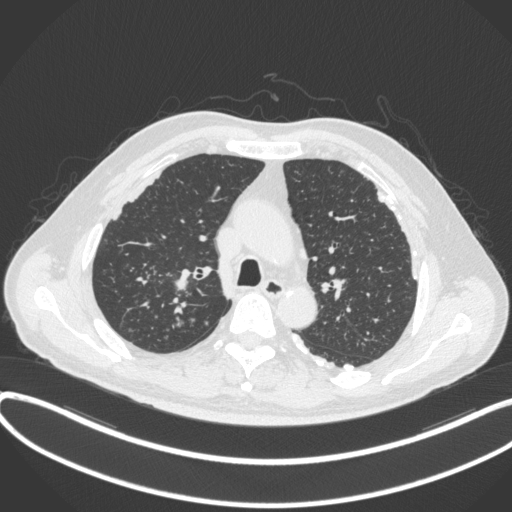
Chest CT, one axial slice. Slice 297 of 455 in the series (ordered by position). Reconstruction kernel B31f. 120 kVp. Lung window (W 1500 / L -600 HU). 1 mm slice thickness. 512 × 512 image matrix. Male patient, age 58 years. Case-level facts recorded for this patient, not image findings: clinical TNM (as recorded): T1c N0 M0.
Structures marked on this image (rectangle marked by the reading radiologist):
- lung tumour (recorded histology: squamous cell carcinoma): bounding box <165,263,195,299> (left, top, right, bottom; pixels)